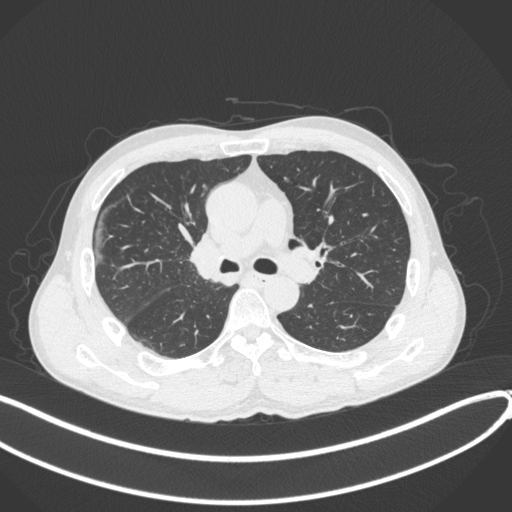
Chest CT, one axial slice. Position 237 of 409 along the scan axis. Lung window (W 1500 / L -600 HU). 512 × 512 image matrix. Male patient, age 53 years. From the clinical record (not read from this slice): clinical TNM (as recorded): T1b N0 M0.
Annotated regions visible in this slice (rectangle marked by the reading radiologist):
- lung tumour (recorded histology: squamous cell carcinoma): bounding box (x1, y1, x2, y2) in pixels: (183, 230, 223, 286)